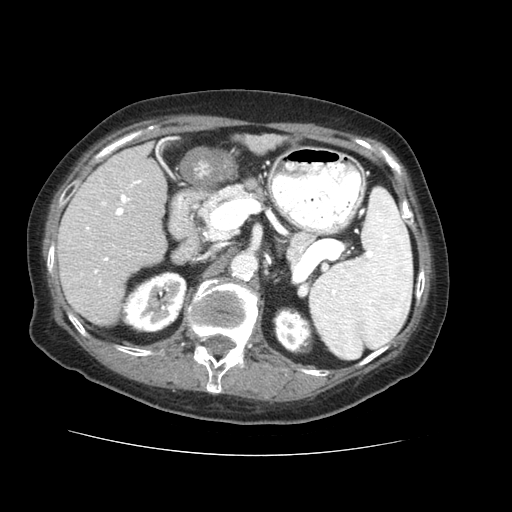
Contrast-enhanced abdominal CT (liver protocol), one axial slice; slice 25 of 73 in the series (ordered by position); reconstruction kernel STANDARD; 120 kVp; soft-tissue window (W 400 / L 40 HU); 512 × 512 image matrix, field of view 360 × 360 mm. From the clinical record (not read from this slice): diagnosis: hepatocellular carcinoma (patient treated with transarterial chemoembolisation; whether this scan precedes or follows treatment is not stated here); TNM stage (as recorded): Stage-IVB; Child-Pugh class: A; tumour differentiation: well differentiated; tumour nodularity: uninodular.
Annotated regions visible in this slice (semi-automatic segmentation, software-assisted and operator-edited):
- liver parenchyma outside the tumour (the mass and vessels are separate outlines, so this box may not span the whole liver): bounding box <56,134,282,324> (left, top, right, bottom; pixels)
- liver vessels: <81,169,141,285>